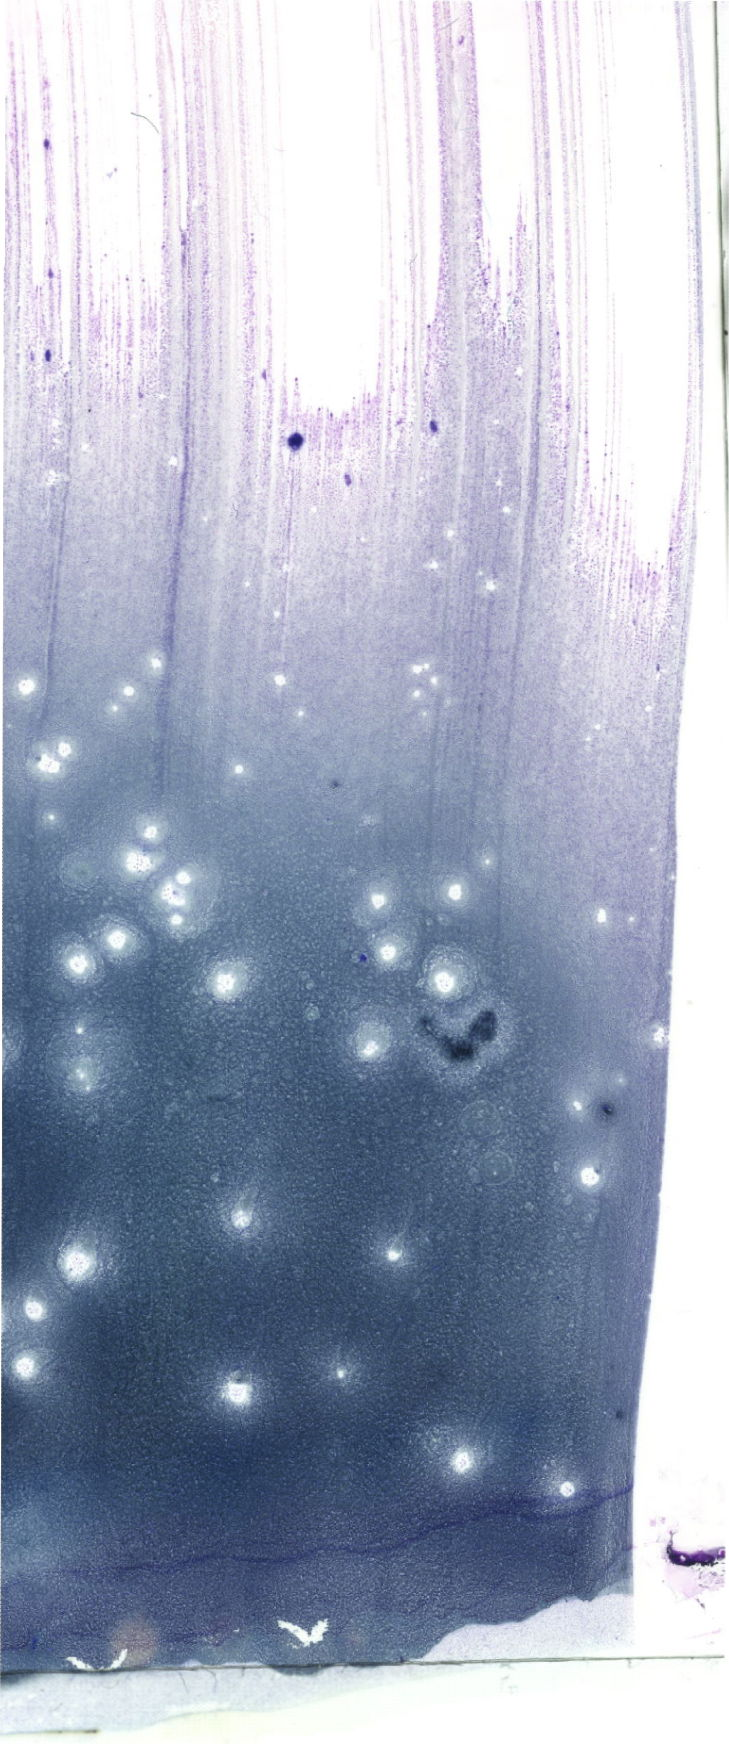
Whole-slide image of a May-Grünwald–Giemsa-stained bone marrow aspirate smear, a low-resolution overview of the entire scanned area, about 20.7 x 49.4 mm.
* diagnosis: Burkitt Leukemia